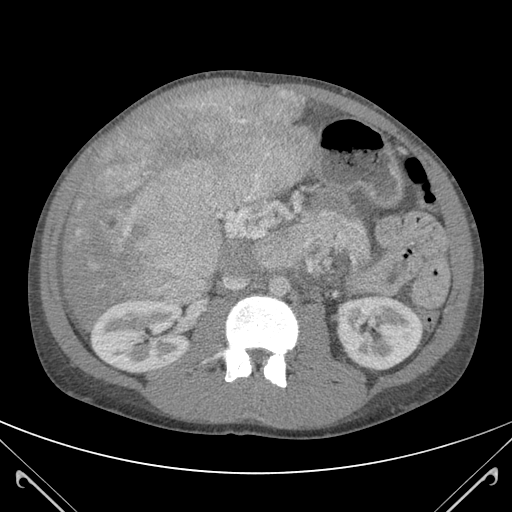
Contrast-enhanced abdominal CT (liver protocol), one axial slice. Position 54 of 118 along the scan axis. 120 kVp. Soft-tissue window (W 400 / L 40 HU). 3 mm slice thickness. 512 × 512 image matrix. From the clinical record (not read from this slice): diagnosis: hepatocellular carcinoma (patient treated with transarterial chemoembolisation; whether this scan precedes or follows treatment is not stated here); TNM stage (as recorded): Stage-IIIB; Child-Pugh class: A.
Outlined on this slice (semi-automatically segmented with operator editing):
- abdominal aorta: box from (x=269, y=277) to (x=289, y=297) px
- liver parenchyma outside the tumour (the mass and vessels are separate outlines, so this box may not span the whole liver): (x=58, y=85)–(x=320, y=324)
- mass: (x=75, y=87)–(x=317, y=304)
- liver vessels: (x=76, y=105)–(x=279, y=290)